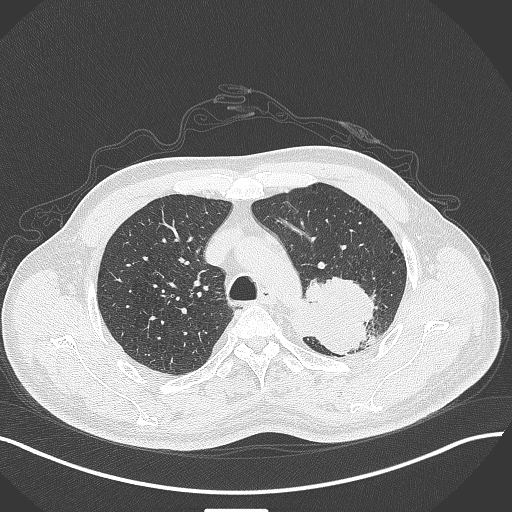
Chest CT, one axial slice. Slice 323 of 429 in the series (ordered by position). Reconstruction kernel B70f. 120 kVp. Lung window (W 1500 / L -600 HU). 512 × 512 image matrix, field of view 400 × 400 mm. Male patient, age 55 years. From the clinical record (not read from this slice): clinical TNM (as recorded): T3 N0 M1c.
Structures marked on this image (bounding box drawn by a radiologist):
- lung tumour (recorded histology: adenocarcinoma): bounding box [x1, y1, x2, y2] px = [288, 271, 384, 354]